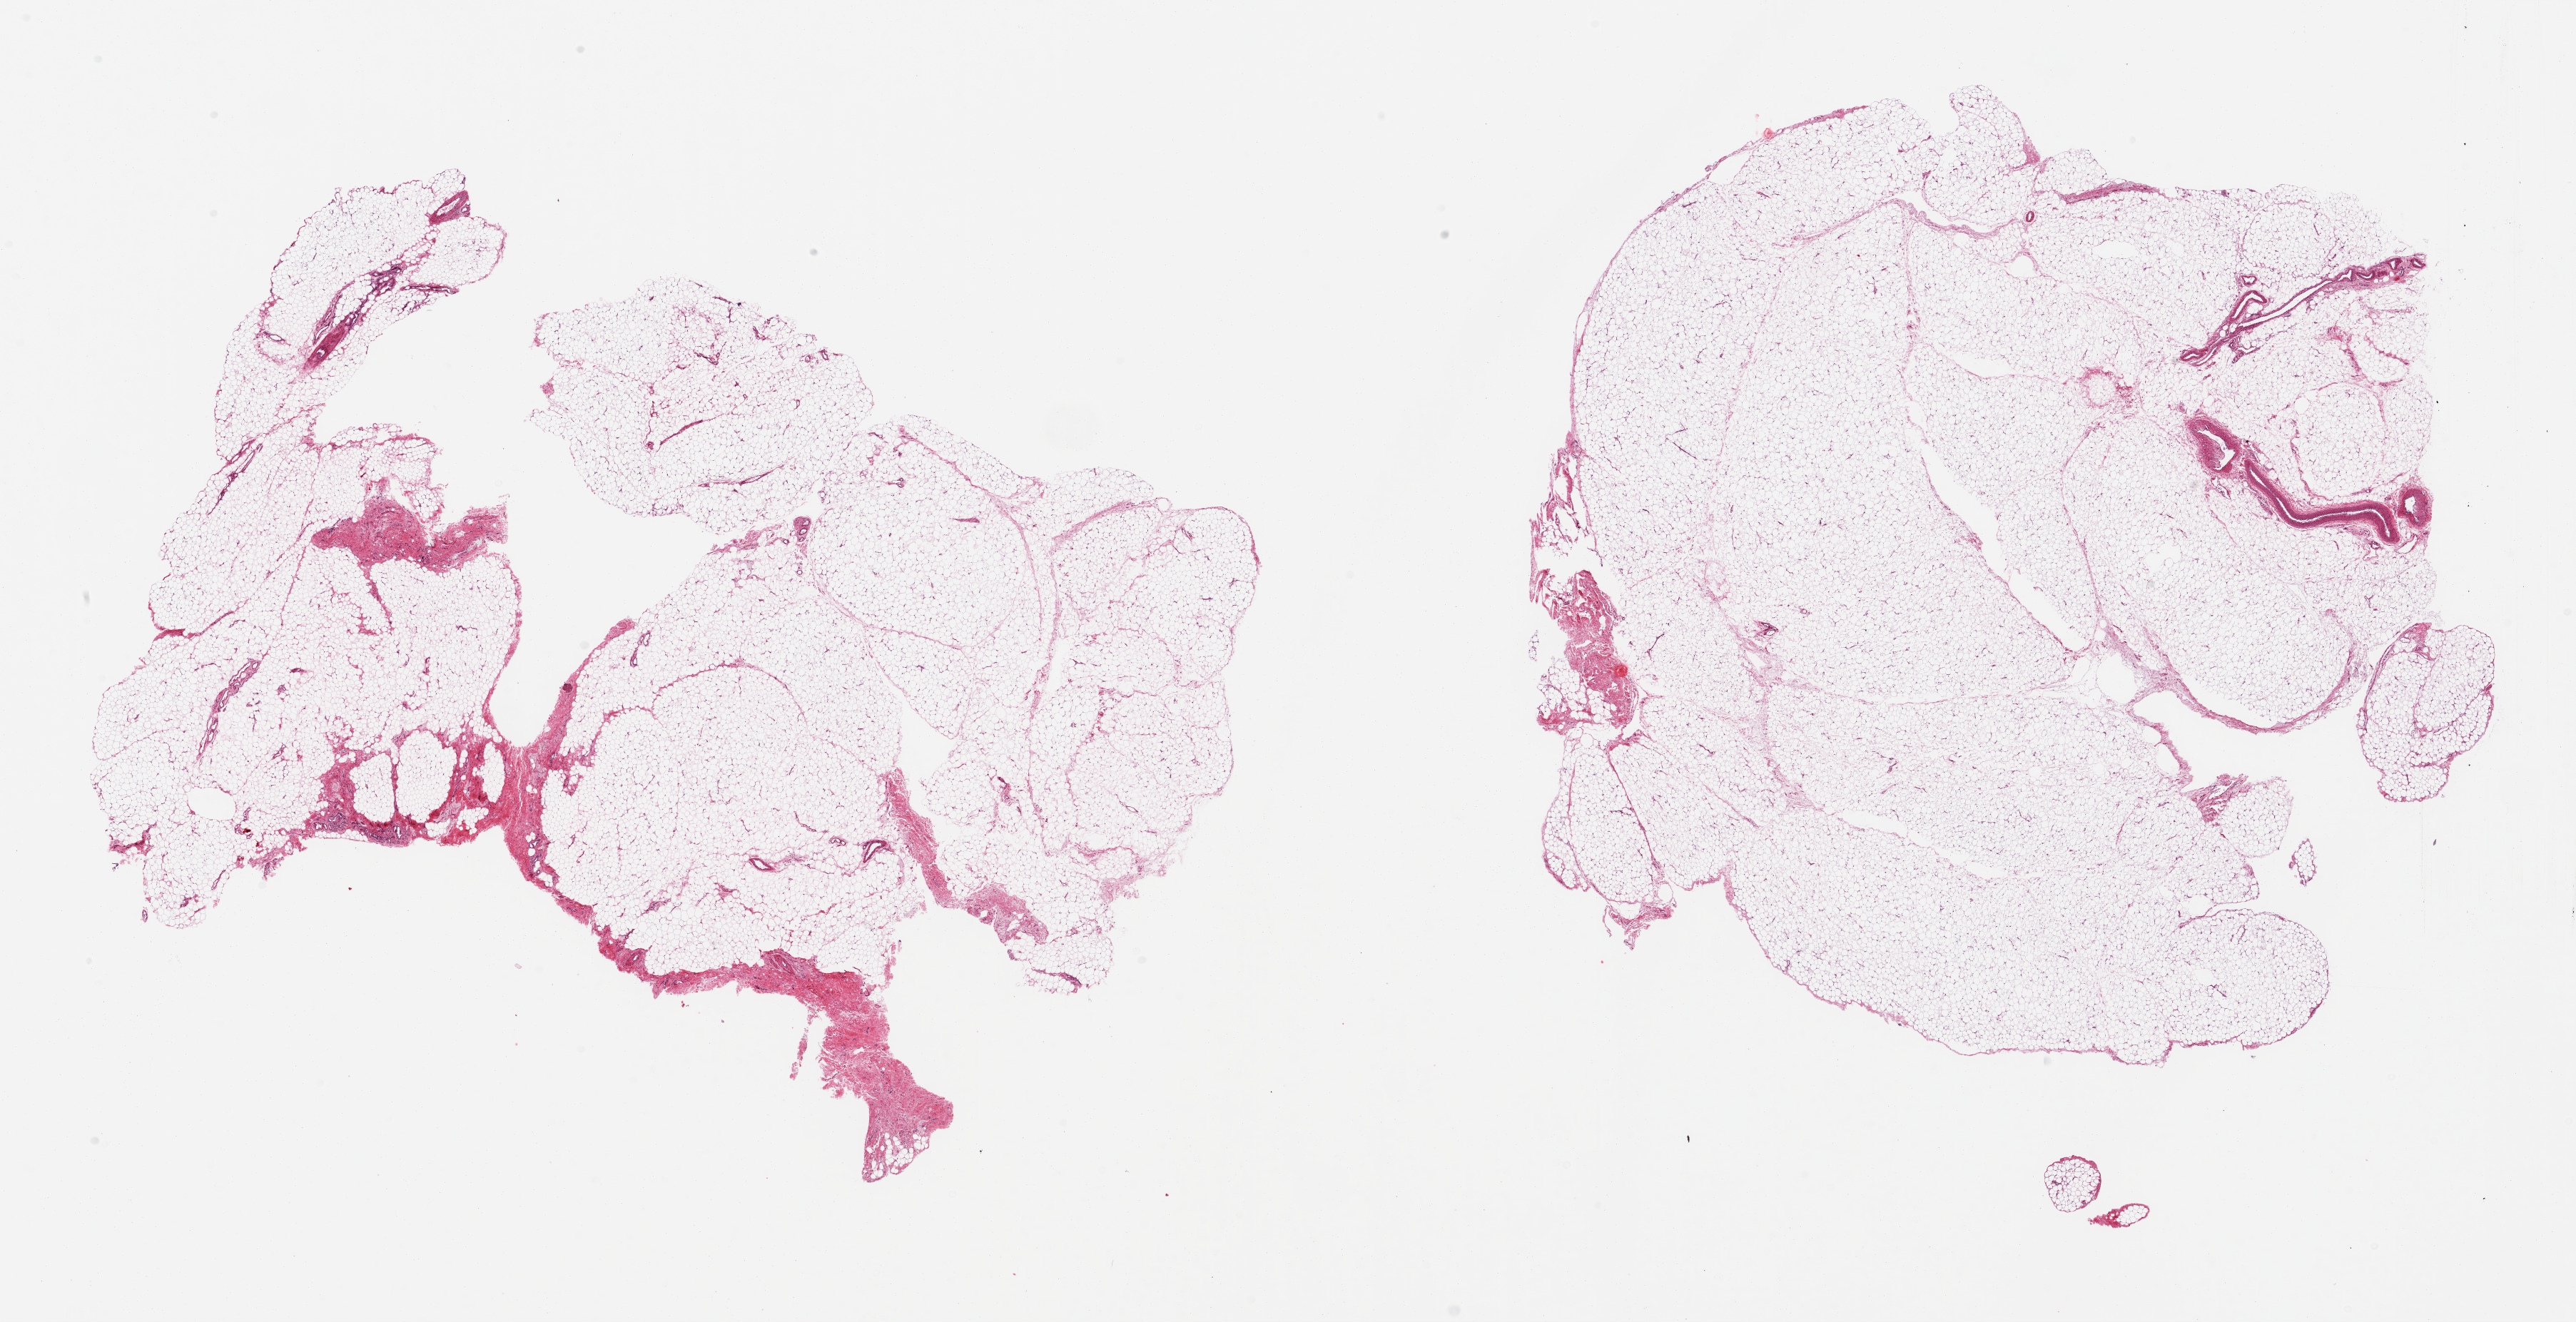
Haematoxylin and eosin whole-slide image, low-resolution overview of the scanned area, about 28.5 x 14.7 mm. PAXgene-fixed, paraffin-embedded tissue. Sampled site (target tissue): omentum. Tissue donor sample. Female donor.
Review note (as recorded): 2 pieces; 5% fibrovascular content.